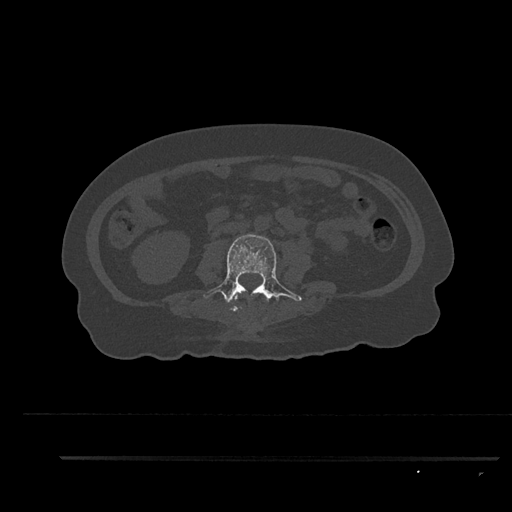
CT including the spine, one axial slice. Position 96 of 797 along the scan axis. Reconstruction kernel Br40s/3. Bone window (W 1800 / L 400 HU). 512 × 512 image matrix, field of view 408 × 408 mm. Patient: female, 44 years. Case-level facts recorded for this patient, not image findings: primary cancer: renal; vertebrae with lytic lesions (as recorded): L1.
Outlined on this slice (semi-automatically segmented with operator editing):
- L2 vertebra: box from (x=231, y=295) to (x=242, y=312) px
- L3 vertebra: (x=203, y=234)–(x=302, y=312)